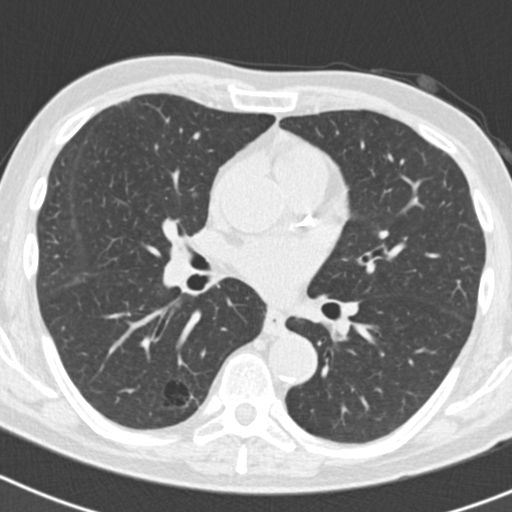
Low-dose screening chest CT, axial slice; second screening round (one year after baseline); lung window (W 1500 / L -600 HU); slice 85 of 186 in the series; 512 × 512 image matrix, field of view 300 × 300 mm. Male, age 70 years at enrolment.
Expert reader's lesion annotation, box from (x=129, y=368) to (x=202, y=432) px. The screening reader recorded 5 non-calcified nodules or masses ≥4 mm on this exam (right lower lobe, right lower lobe, right upper lobe, right upper lobe, left upper lobe); which of them this box marks is not recorded. Later outcome: lung cancer diagnosed 622 days after this screen — bronchiolo-alveolar adenocarcinoma, NOS, right lower lobe, poorly differentiated (G3), stage IB (AJCC 6th edition), 30 mm at pathology.